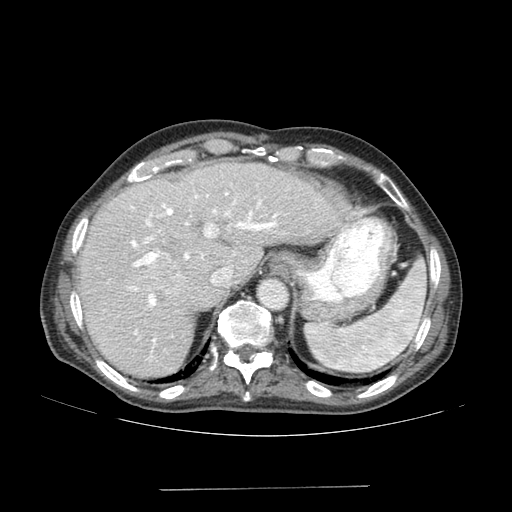
Contrast-enhanced abdominal CT (liver protocol), one axial slice. Slice 120 of 192 in the series (ordered by position). Reconstruction kernel SOFT. 120 kVp. Soft-tissue window (W 400 / L 40 HU). 2.5 mm slice thickness. 512 × 512 image matrix, field of view 400 × 400 mm. From the clinical record (not read from this slice): diagnosis: hepatocellular carcinoma (patient treated with transarterial chemoembolisation; whether this scan precedes or follows treatment is not stated here); TNM stage (as recorded): Stage-IVA.
Outlined on this slice (semi-automatic segmentation, software-assisted and operator-edited):
- liver parenchyma outside the tumour (the mass and vessels are separate outlines, so this box may not span the whole liver): bounding box <78,162,356,376> (left, top, right, bottom; pixels)
- mass: <134,258,188,296>
- liver vessels: <129,192,278,344>